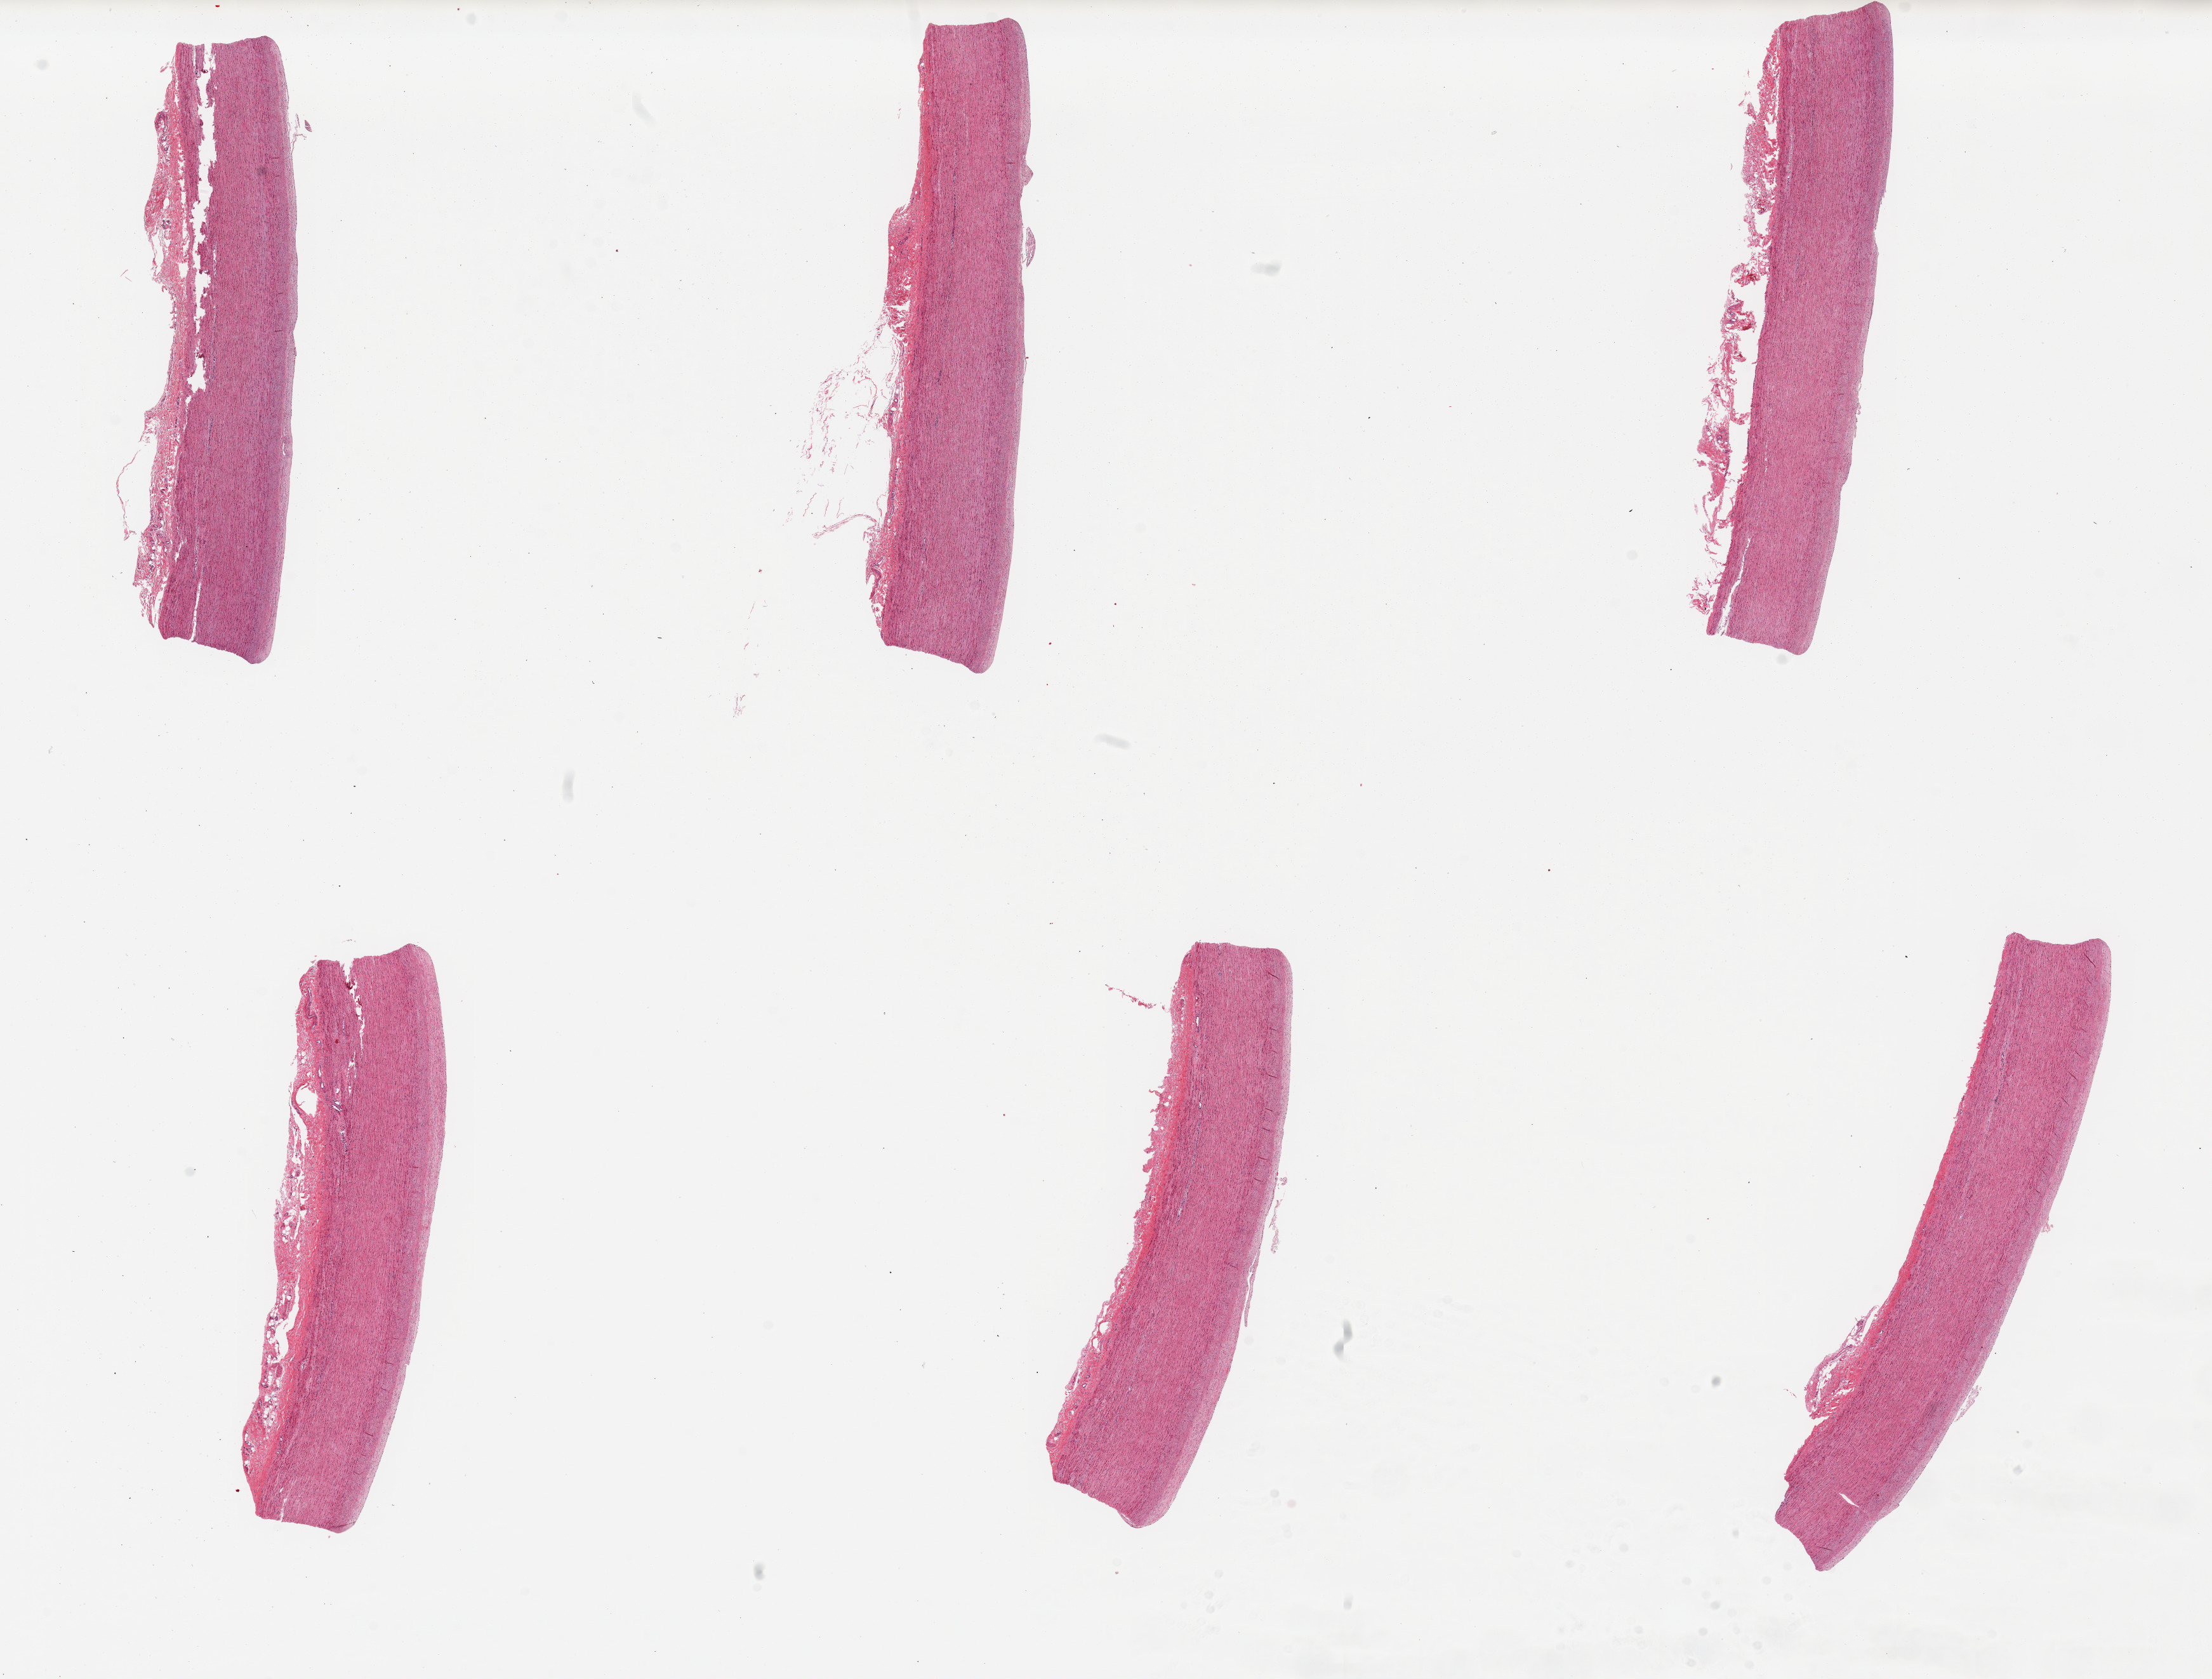
Hematoxylin and eosin (H&E) whole-slide image — a low-resolution overview of the entire scanned area, about 27.6 x 20.9 mm; PAXgene-fixed, paraffin-embedded tissue; target tissue: aorta; tissue donor sample. Donor: male.
- reviewer comment on this tissue sample: 6 pieces, up to 9x1.5mm; minimal plaque; adipose ee adventitia